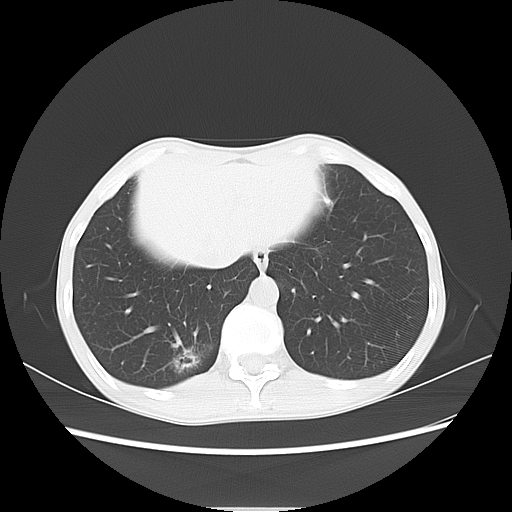
Chest CT, one axial slice. Position 17 of 69 along the scan axis. Reconstruction kernel LUNG. 120 kVp. Lung window (W 1500 / L -600 HU). 5 mm slice thickness. 512 × 512 image matrix, field of view 350 × 350 mm. Female patient, age 51 years. From the clinical record (not read from this slice): clinical TNM (as recorded): T1c N0 M0; histopathological grade: G2-3.
Annotated regions visible in this slice (bounding box drawn by a radiologist):
- lung tumour (recorded histology: adenocarcinoma): bounding box (x1, y1, x2, y2) in pixels: (163, 337, 216, 382)